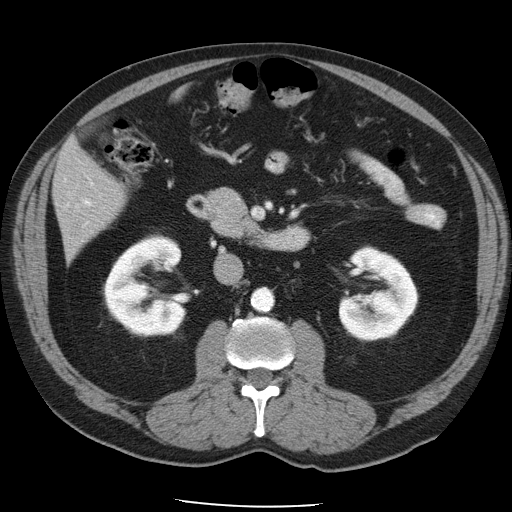
Contrast-enhanced abdominal CT, one axial slice. Slice 19 of 49 in the series (ordered by position). Intravenous contrast given. Soft-tissue window (W 400 / L 40 HU). 5 mm slice thickness. 512 × 512 image matrix. Male patient, age 68 years. Case-level facts recorded for this patient, not image findings: diagnosis: colorectal cancer liver metastases, imaged before liver resection; multiple liver metastases: yes; largest metastasis: 1.7 cm.
Outlined on this slice (expert manual segmentation):
- liver: box from (x=54, y=139) to (x=123, y=255) px
- planned liver remnant (the part of the liver to remain after resection): (x=60, y=139)–(x=124, y=207)
- portal vein (with intrahepatic branches): (x=65, y=180)–(x=92, y=224)
- liver metastasis: (x=67, y=219)–(x=83, y=235)